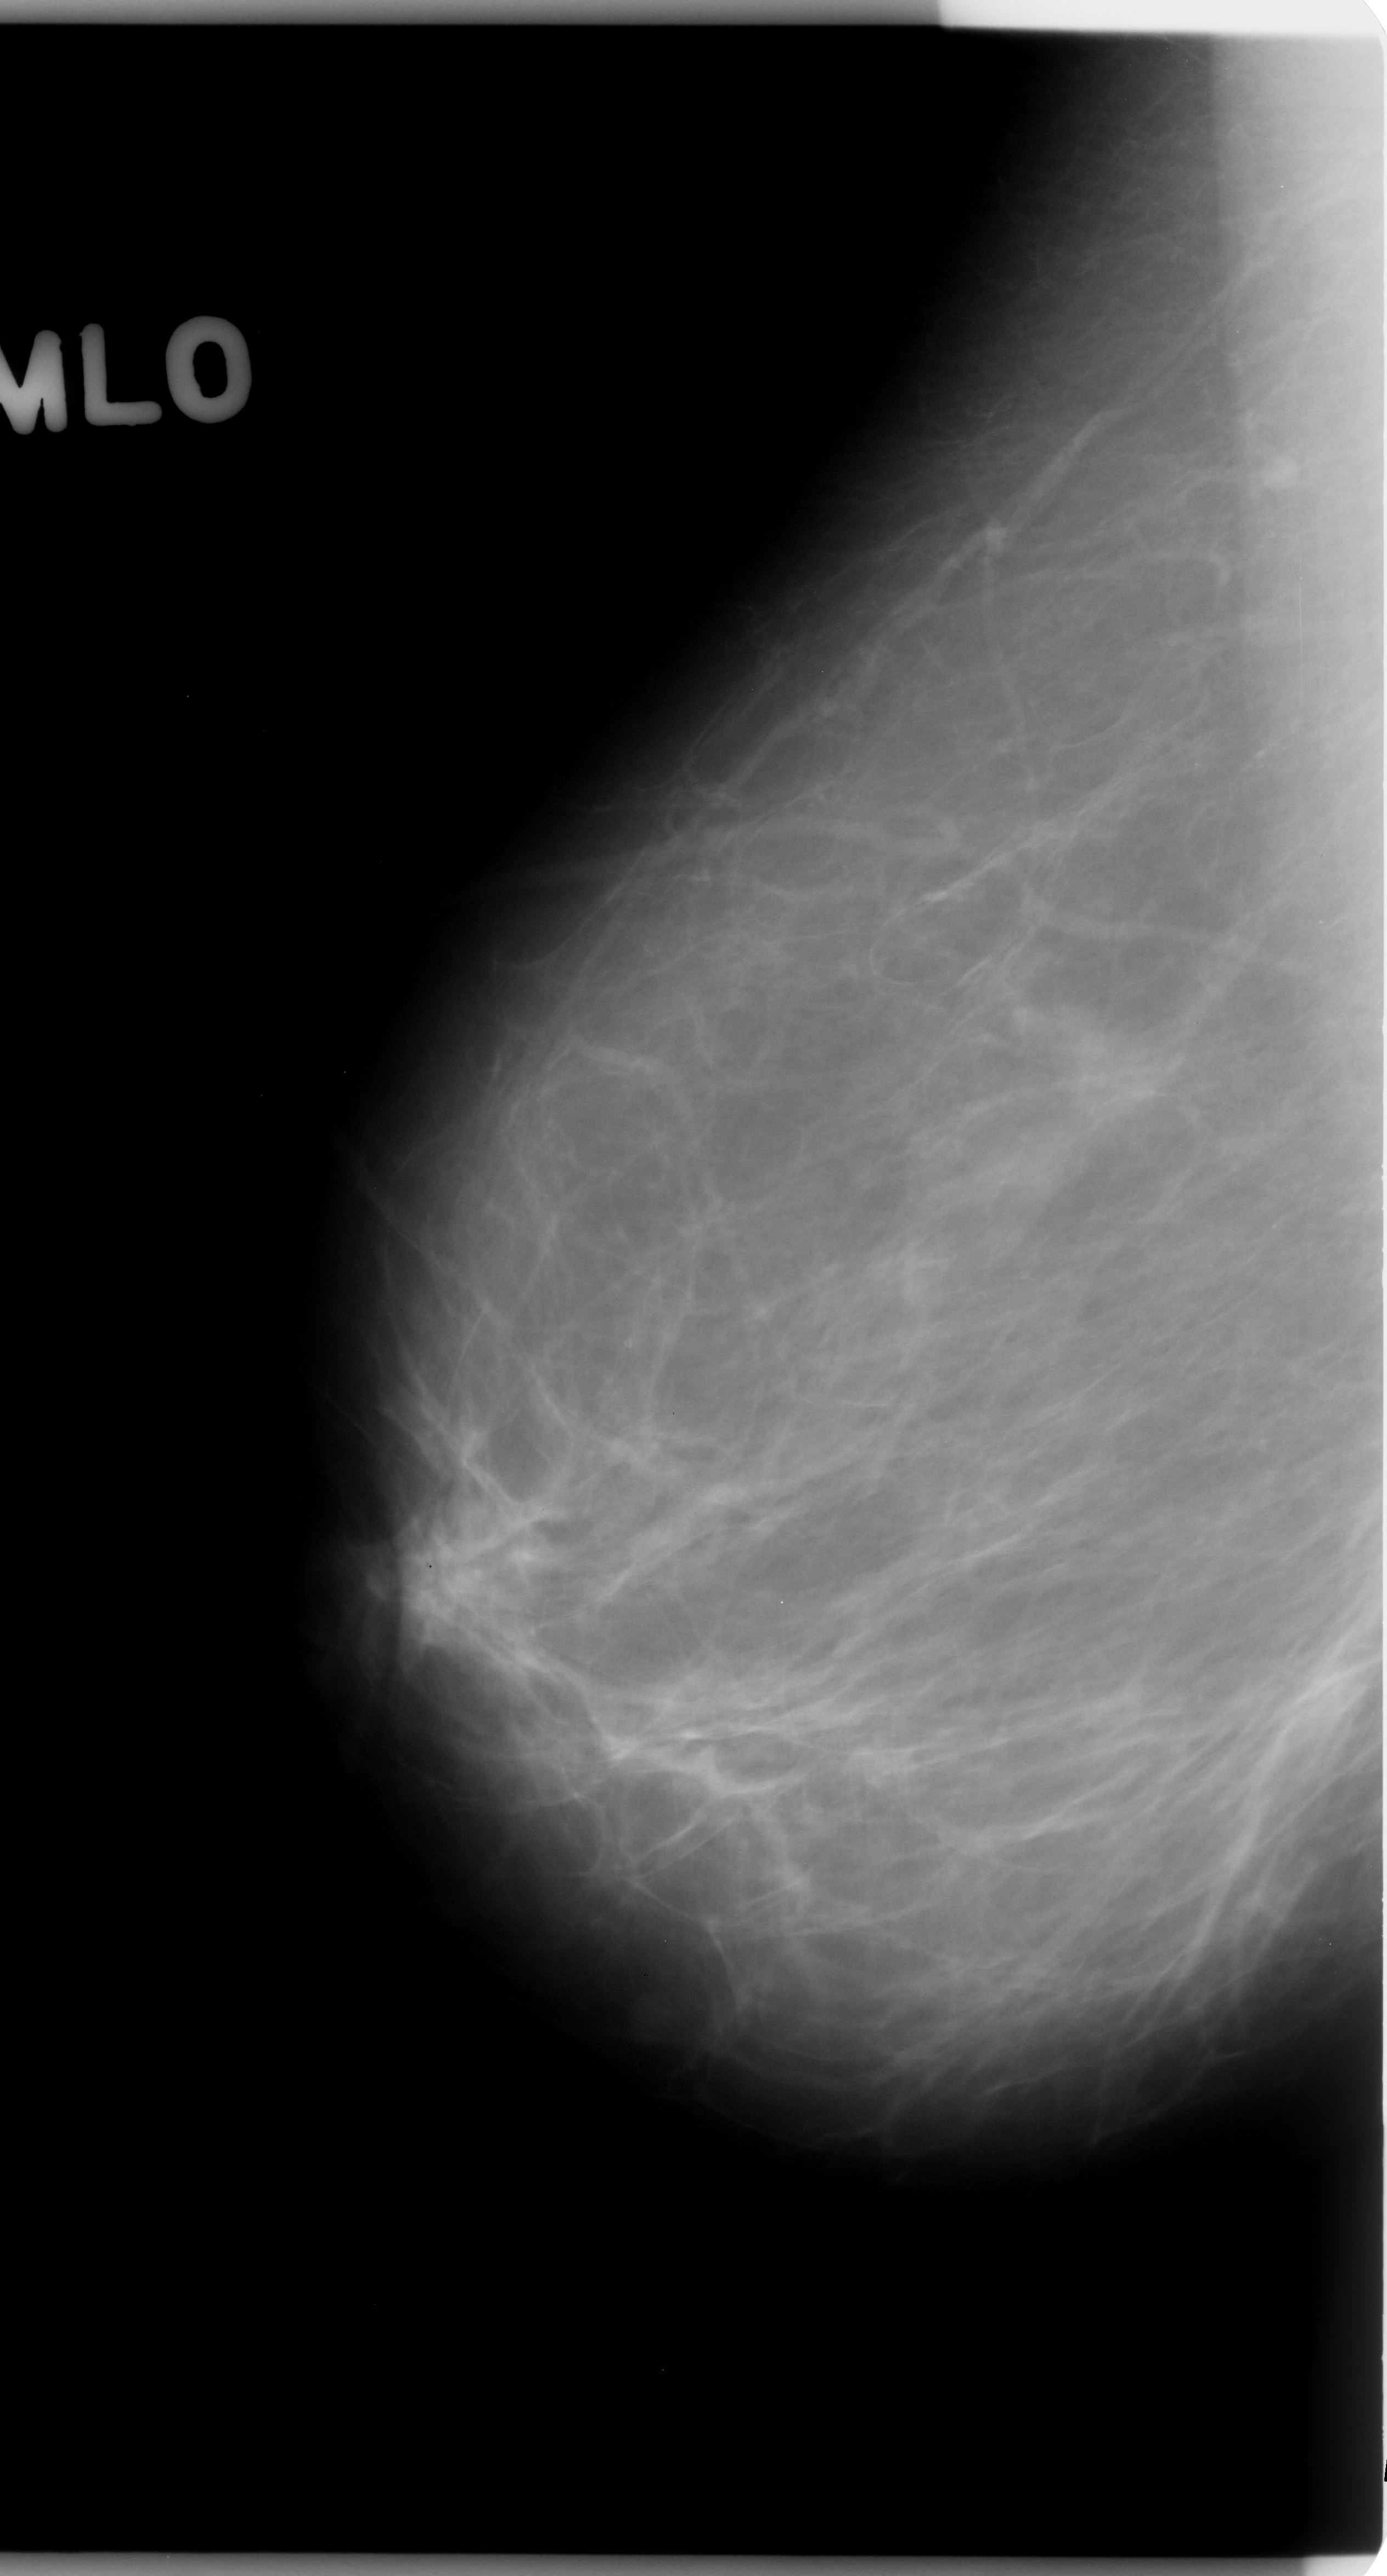
Mammogram (digitized film); right breast; mediolateral oblique (MLO) view; 1387 × 2576 image matrix.
Expert-marked regions of interest on this image (one box per marked abnormality):
- mass, shape lobulated, margins ill defined; BI-RADS assessment category 5; pathology result (as recorded, not read from the image): malignant: bounding box <392,1472,568,1630> (left, top, right, bottom; pixels)